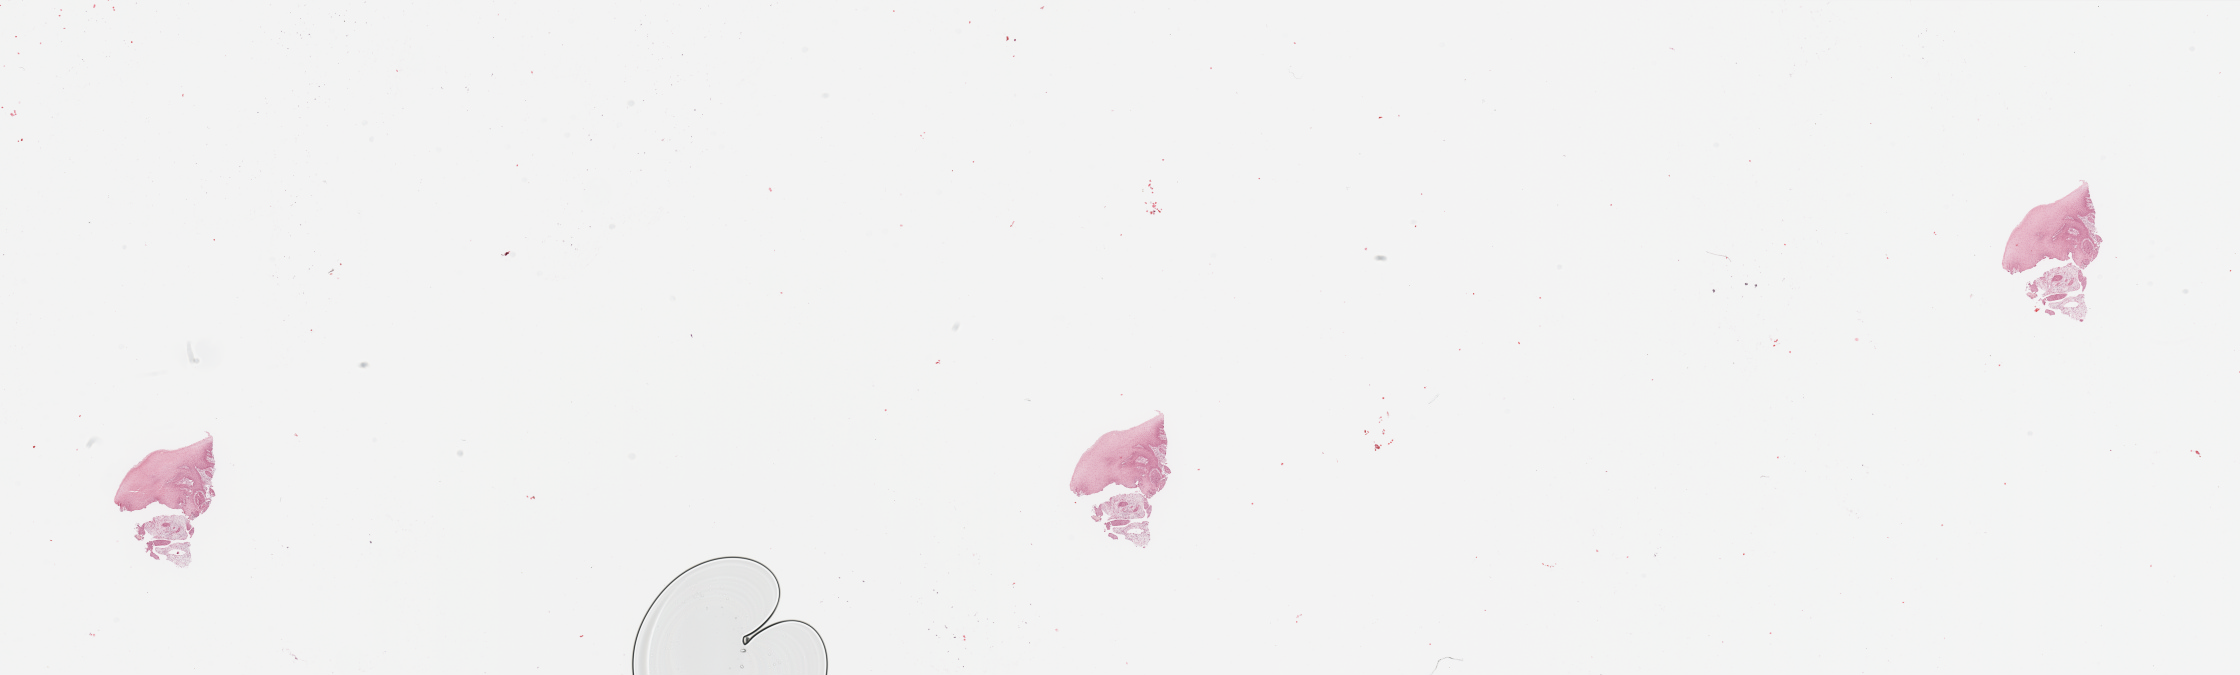
H&E-stained whole-slide image — low-resolution overview of the scanned area, about 35.4 x 10.7 mm, tumour tissue sample, sampled site: floor of mouth. 58-year-old male patient. Histologic grade: G2 (moderately differentiated). Pathologist review of this section (percent, as recorded): tumour nuclei 80%, necrosis 0%.
Histologic diagnosis: Squamous cell carcinoma, NOS (floor of mouth, NOS). Primary tumour site (as recorded): oral cavity. AJCC pathologic stage: I.